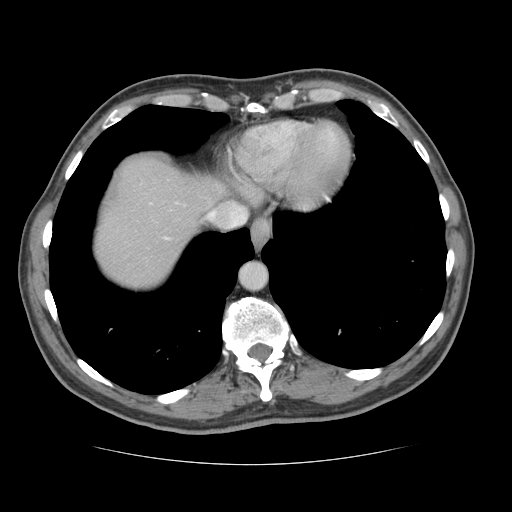
Contrast-enhanced abdominal CT, one axial slice; slice 117 of 134 in the series (ordered by position); reconstruction kernel STANDARD; intravenous contrast given; soft-tissue window (W 400 / L 40 HU); 512 × 512 image matrix, field of view 377 × 377 mm. Male patient, age 68 years. From the clinical record (not read from this slice): diagnosis: colorectal cancer liver metastases, imaged before liver resection; multiple liver metastases: yes; largest metastasis: 2.2 cm; disease in both lobes: no.
Outlined on this slice (expert manual segmentation):
- hepatic veins: bounding box (x1, y1, x2, y2) in pixels: (227, 204, 246, 214)
- liver: (95, 159, 227, 289)
- planned liver remnant (the part of the liver to remain after resection): (96, 159, 226, 288)